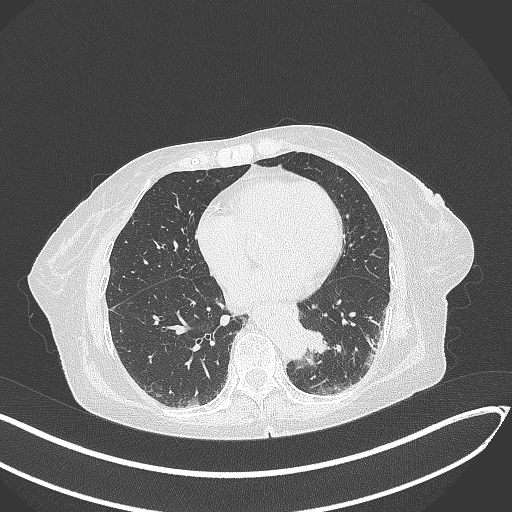
Chest CT, one axial slice. Position 81 of 324 along the scan axis. 120 kVp. Lung window (W 1500 / L -600 HU). 512 × 512 image matrix. Female patient, age 82 years. Case-level facts recorded for this patient, not image findings: clinical TNM (as recorded): T1b N0 M1.
Outlined on this slice (rectangle marked by the reading radiologist):
- lung tumour (recorded histology: adenocarcinoma): bounding box (x1, y1, x2, y2) in pixels: (301, 325, 332, 356)